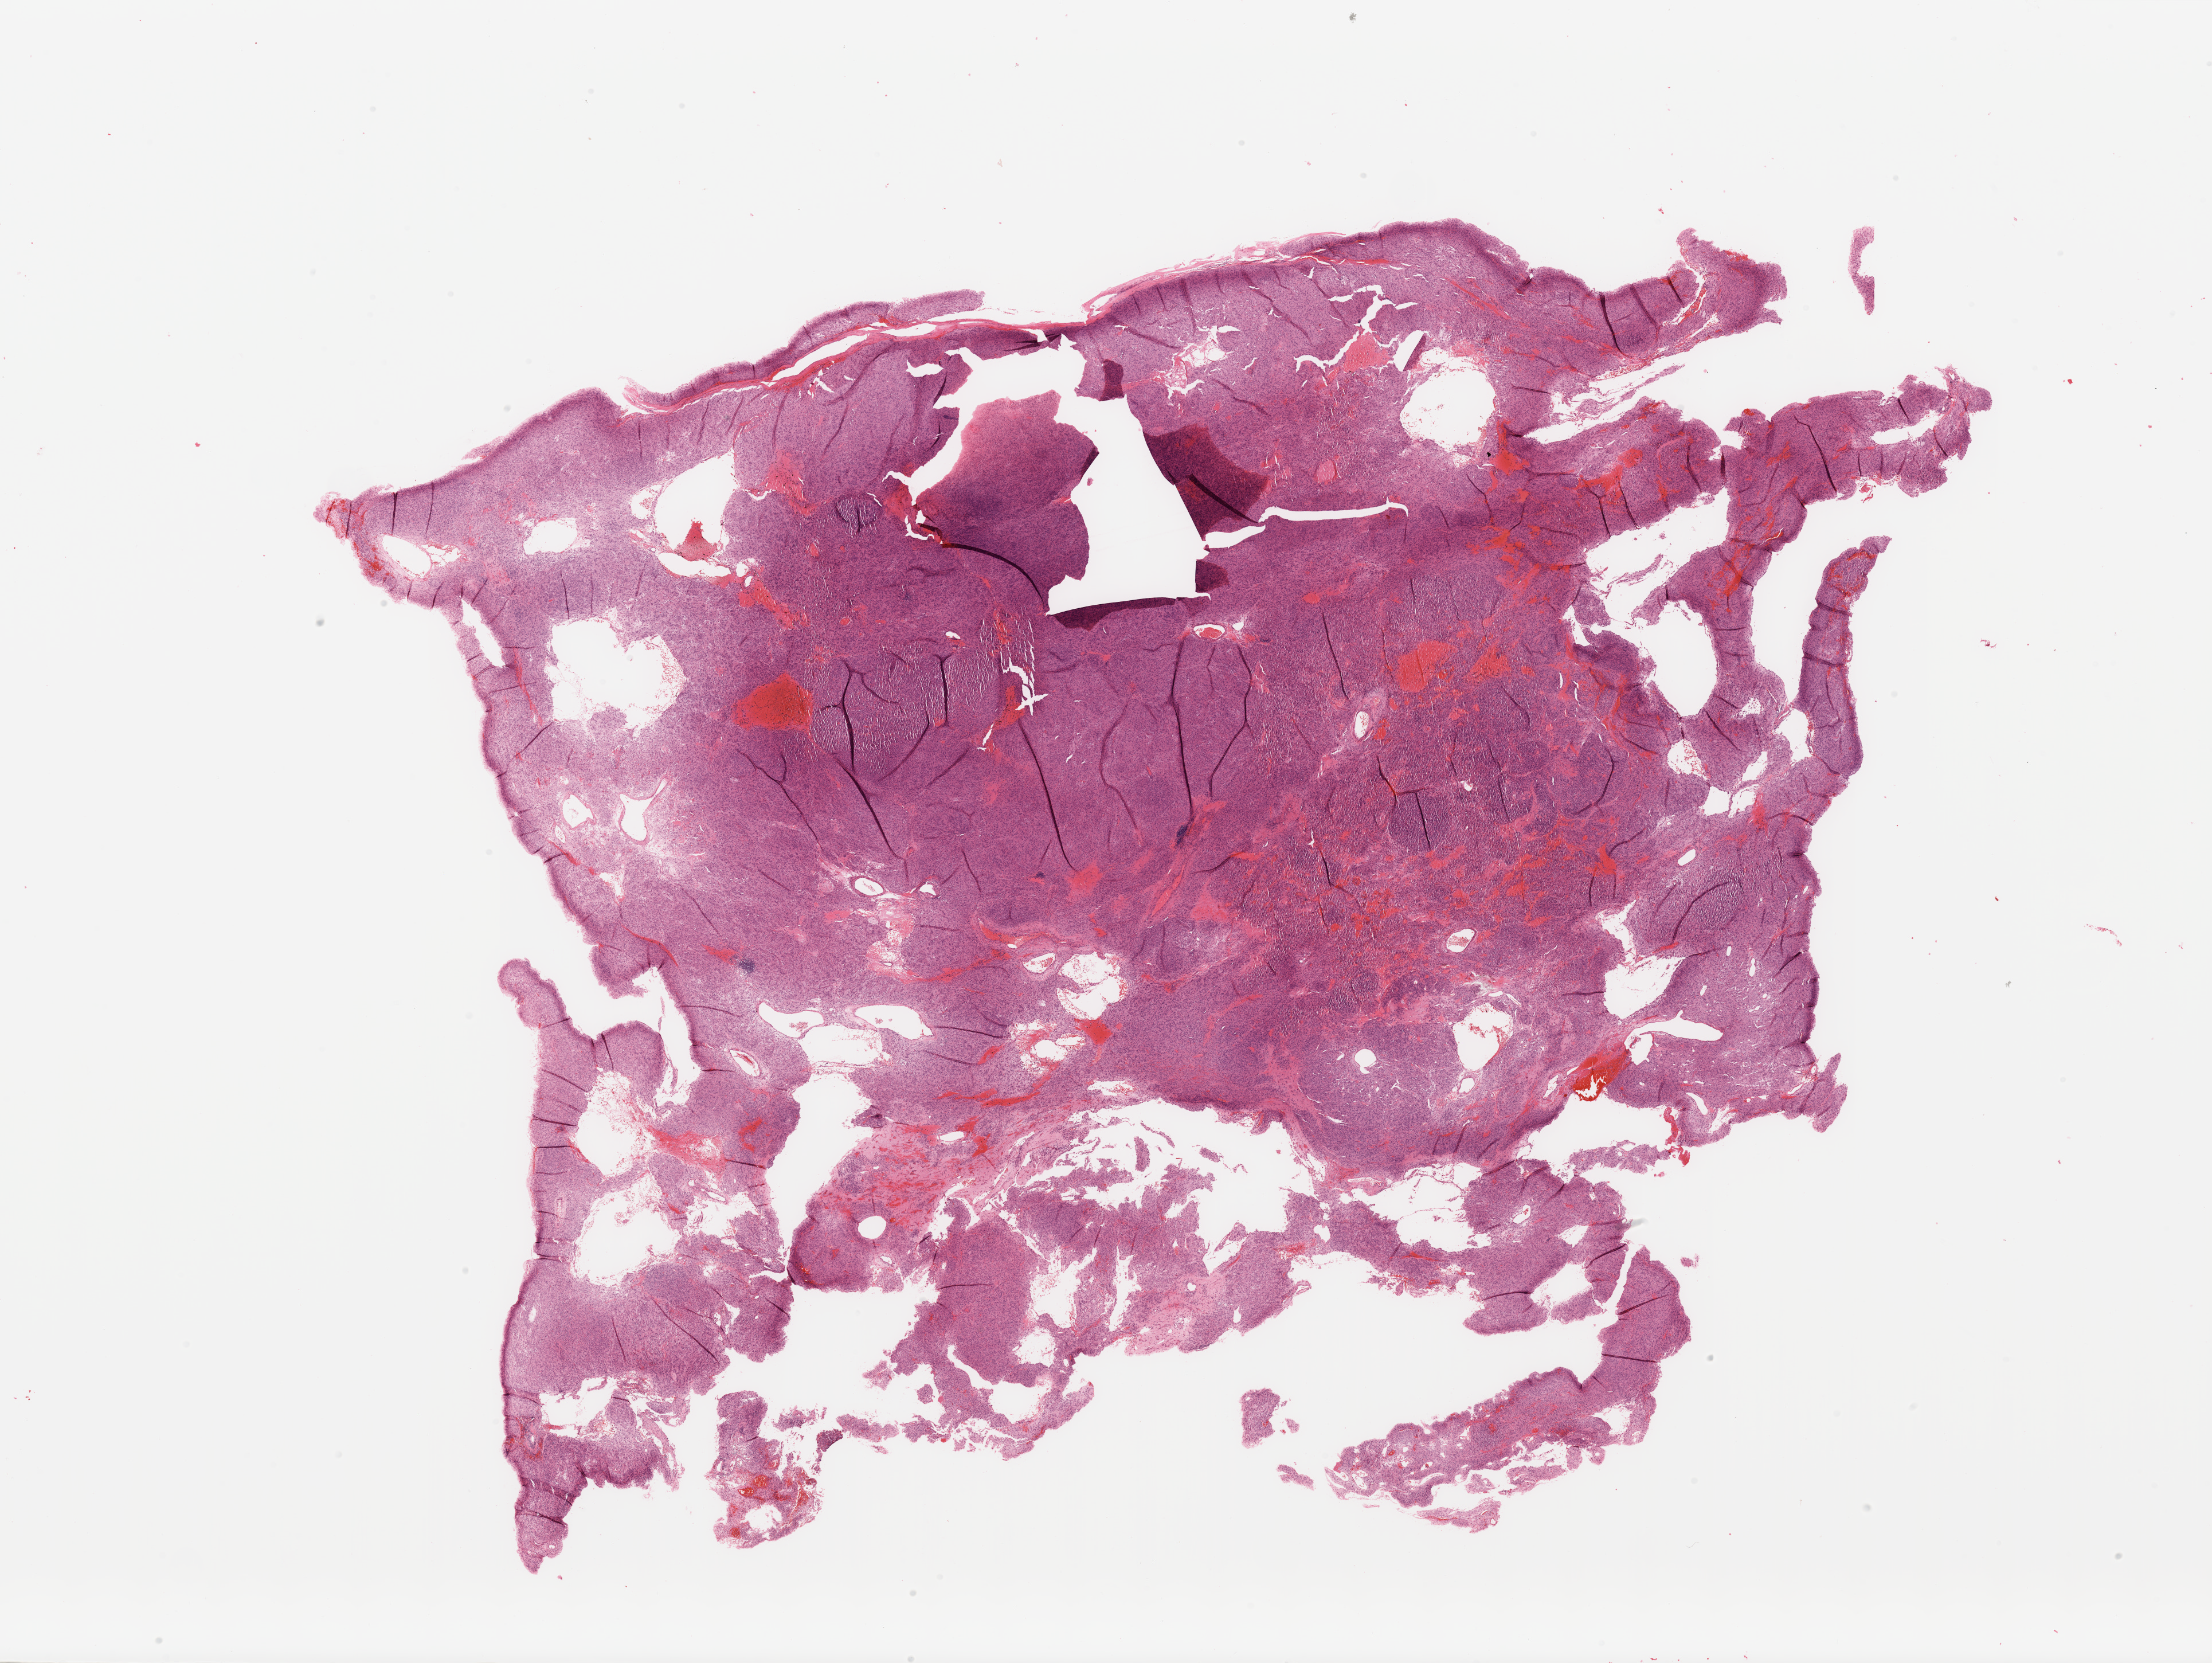
Digitized H&E-stained tissue section (whole slide) — low-resolution overview of the scanned area, about 30.5 x 22.9 mm (slide scanned at 20x). Patient: female, age 73 years.
Patient diagnosis (cohort enrolment): sarcoma (site not recorded at cohort level).